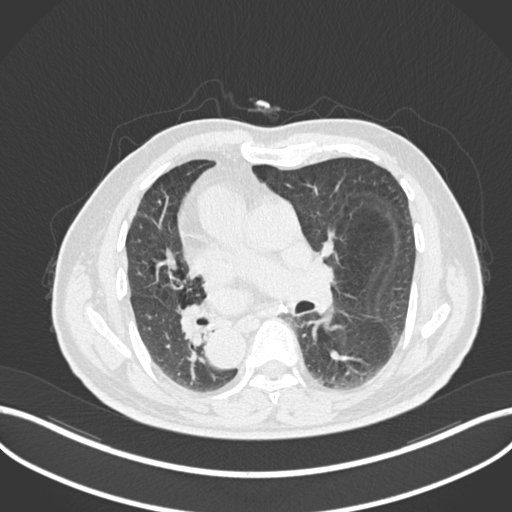
Chest CT, one axial slice; slice 114 of 206 in the series (ordered by position); reconstruction kernel B30f; 120 kVp; lung window (W 1500 / L -600 HU); 1 mm slice thickness; 512 × 512 image matrix. Male patient, age 67 years. From the clinical record (not read from this slice): clinical TNM (as recorded): T2a N0 M0.
Structures marked on this image (bounding box drawn by a radiologist):
- lung tumour (recorded histology: squamous cell carcinoma): bounding box <176,296,210,339> (left, top, right, bottom; pixels)